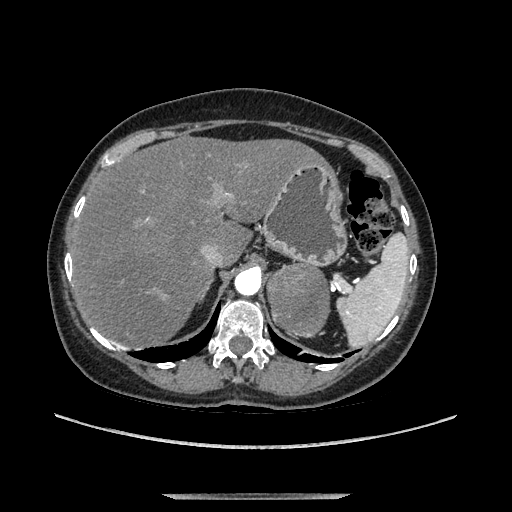
Contrast-enhanced abdominal CT, one axial slice; position 98 of 169 along the scan axis; soft-tissue window (W 400 / L 40 HU); 1.25 mm slice thickness; 512 × 512 image matrix. Female patient. Case-level facts recorded for this patient, not image findings: diagnosis: adrenocortical carcinoma; tumour side: left adrenal; tumour size at pathology: 9 cm; Ki-67 index: 2 %; stage (as recorded): 3.
Structures marked on this image (semi-automatically segmented with operator editing):
- mass: bounding box <270,265,329,336> (left, top, right, bottom; pixels)